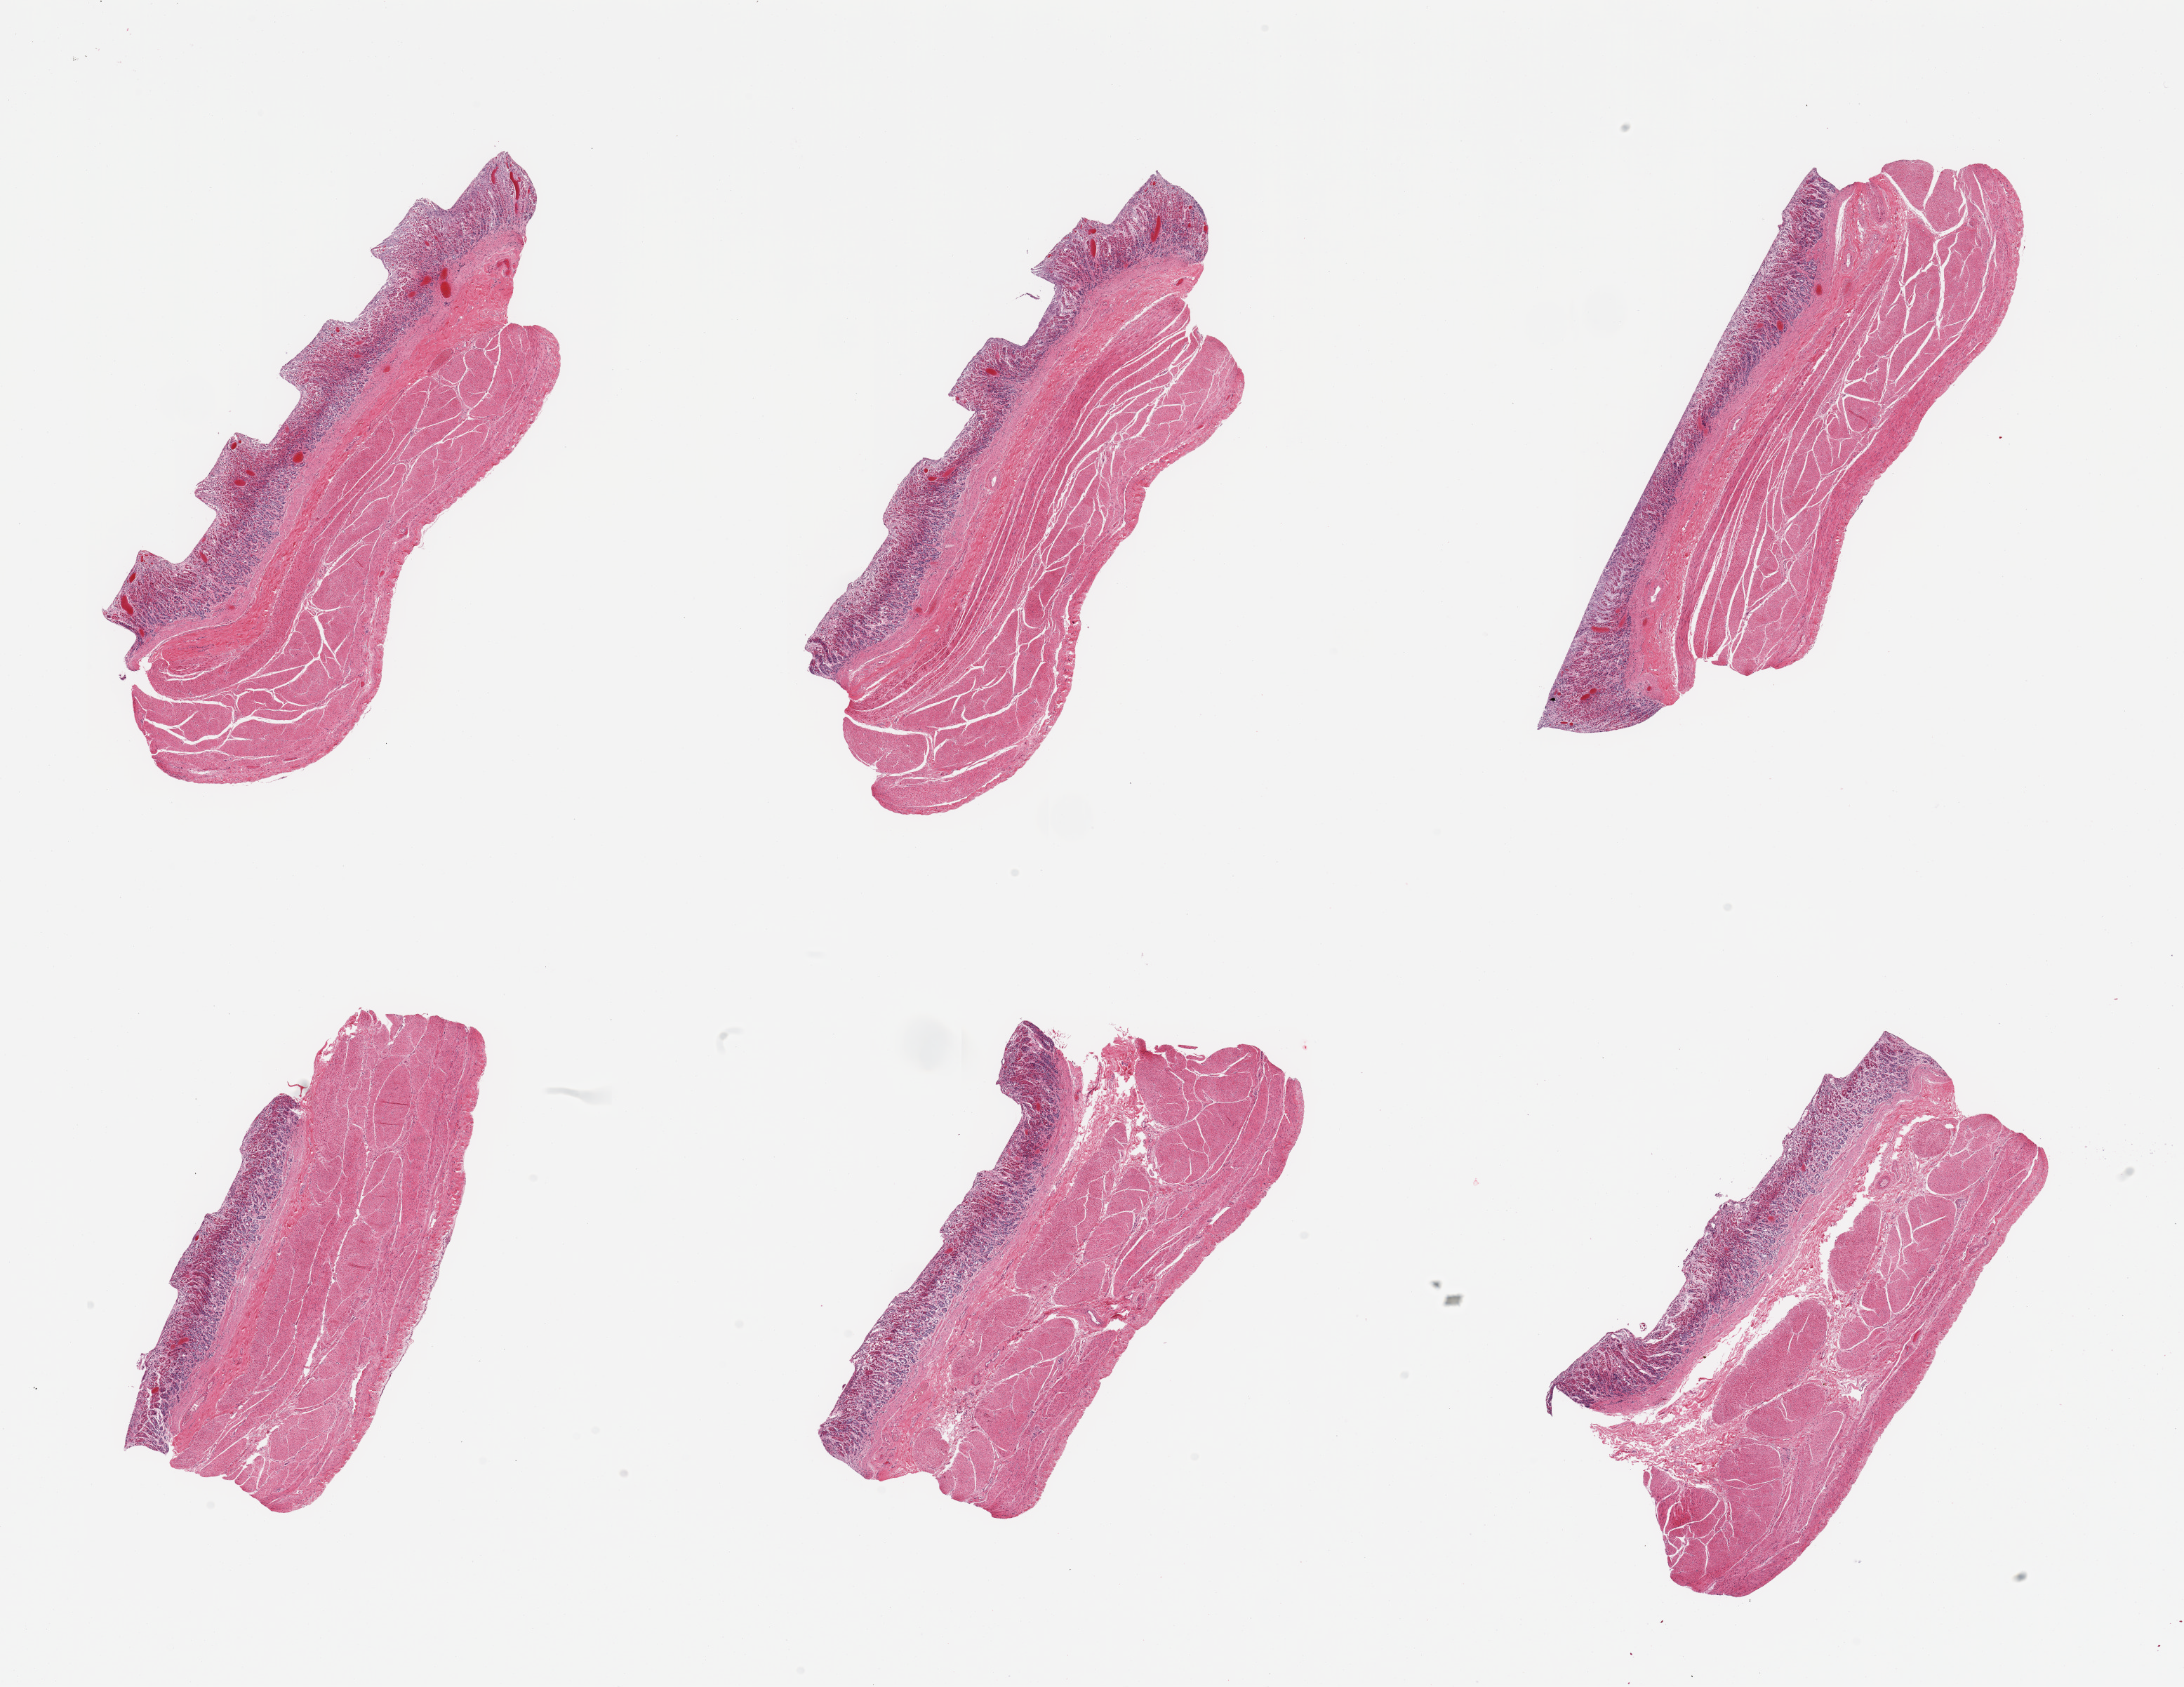
Whole-slide image, H&E stain, low-resolution overview of the scanned area, about 24.6 x 19.0 mm (from a 20x scan). PAXgene-fixed, paraffin-embedded tissue. Section of stomach (target tissue). Donor tissue sample. Donor sex: male.
Review note (as recorded): 6 pieces; full thickness sections, moderate to severe autolysis.